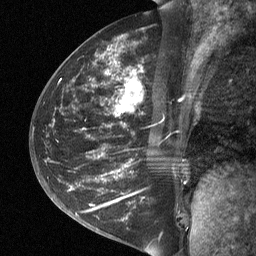
Breast MRI (dynamic contrast-enhanced), one sagittal slice; slice 29 of 64 in the series (ordered by position); dynamic contrast-enhanced study with each time point stored as its own series, time point 2 of 3 at this slice position (early post-contrast, ordered by acquisition time); 1.5 T; TE 4.8 ms, TR 27 ms; 2 mm slice thickness; 256 × 256 image matrix, field of view 200 × 200 mm. Female patient, age 42 years. From the clinical record (not read from this slice): setting: breast cancer imaged before/during neoadjuvant chemotherapy; receptor status: triple-negative.
Structures marked on this image (semi-automatic segmentation, software-assisted and operator-edited):
- analysis volume of interest (the breast-tissue region the enhancement analysis was run in; not a lesion): bounding box <49,45,196,197> (left, top, right, bottom; pixels)
- tumour enhancement mask (voxels above the 90 % enhancement threshold inside the analysis volume of interest): <123,71,136,103>